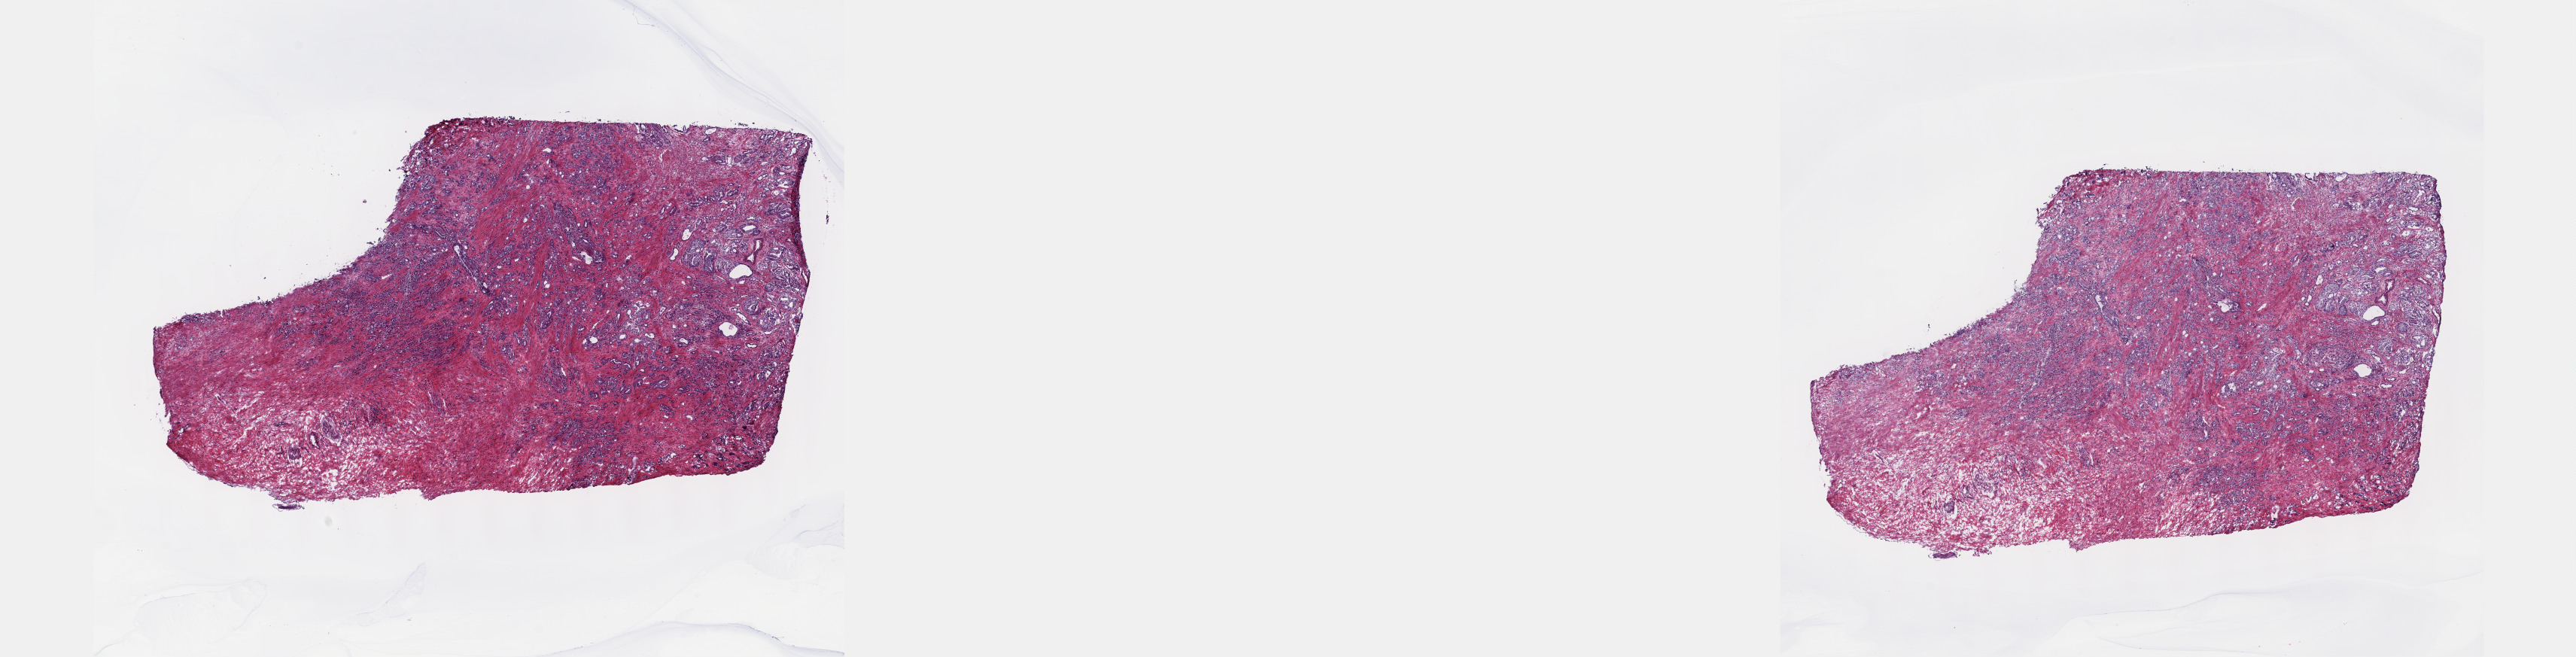
H&E-stained whole-slide image — shown as a low-resolution overview of the whole scanned area (about 27.7 x 7.1 mm, from a 40x scan), frozen section, primary tumour sample from the prostate. Male, age 67 years at initial diagnosis. Gleason score: 9 (4+5). Pathologist review of this section (percent, as recorded): tumour cells 50%, tumour nuclei 60%, normal cells 0%, stromal cells 50%, necrosis 0%. Infiltration values recorded for this section: lymphocyte infiltration 0%, monocyte infiltration 0%, neutrophil infiltration 0%.
Diagnosis: Adenocarcinoma, NOS (prostate gland). Laterality: bilateral.